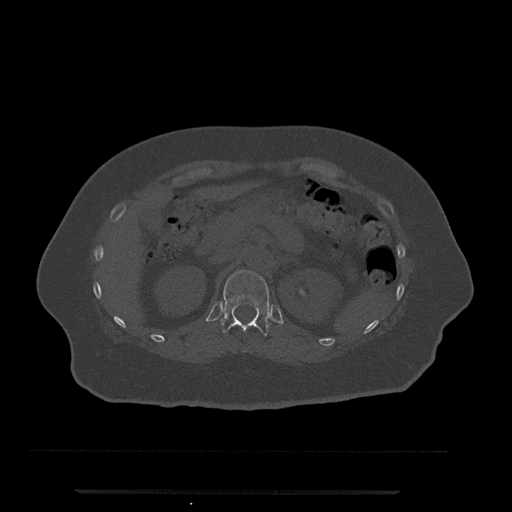
CT including the spine, one axial slice. Slice 172 of 797 in the series (ordered by position). 120 kVp. Bone window (W 1800 / L 400 HU). 0.5 mm slice thickness. 512 × 512 image matrix, field of view 440 × 440 mm. Female patient, age 51 years. Case-level facts recorded for this patient, not image findings: primary cancer: neuro.
Structures marked on this image (semi-automatic segmentation, software-assisted and operator-edited):
- T12 vertebra: bounding box [x1, y1, x2, y2] px = [221, 270, 270, 337]